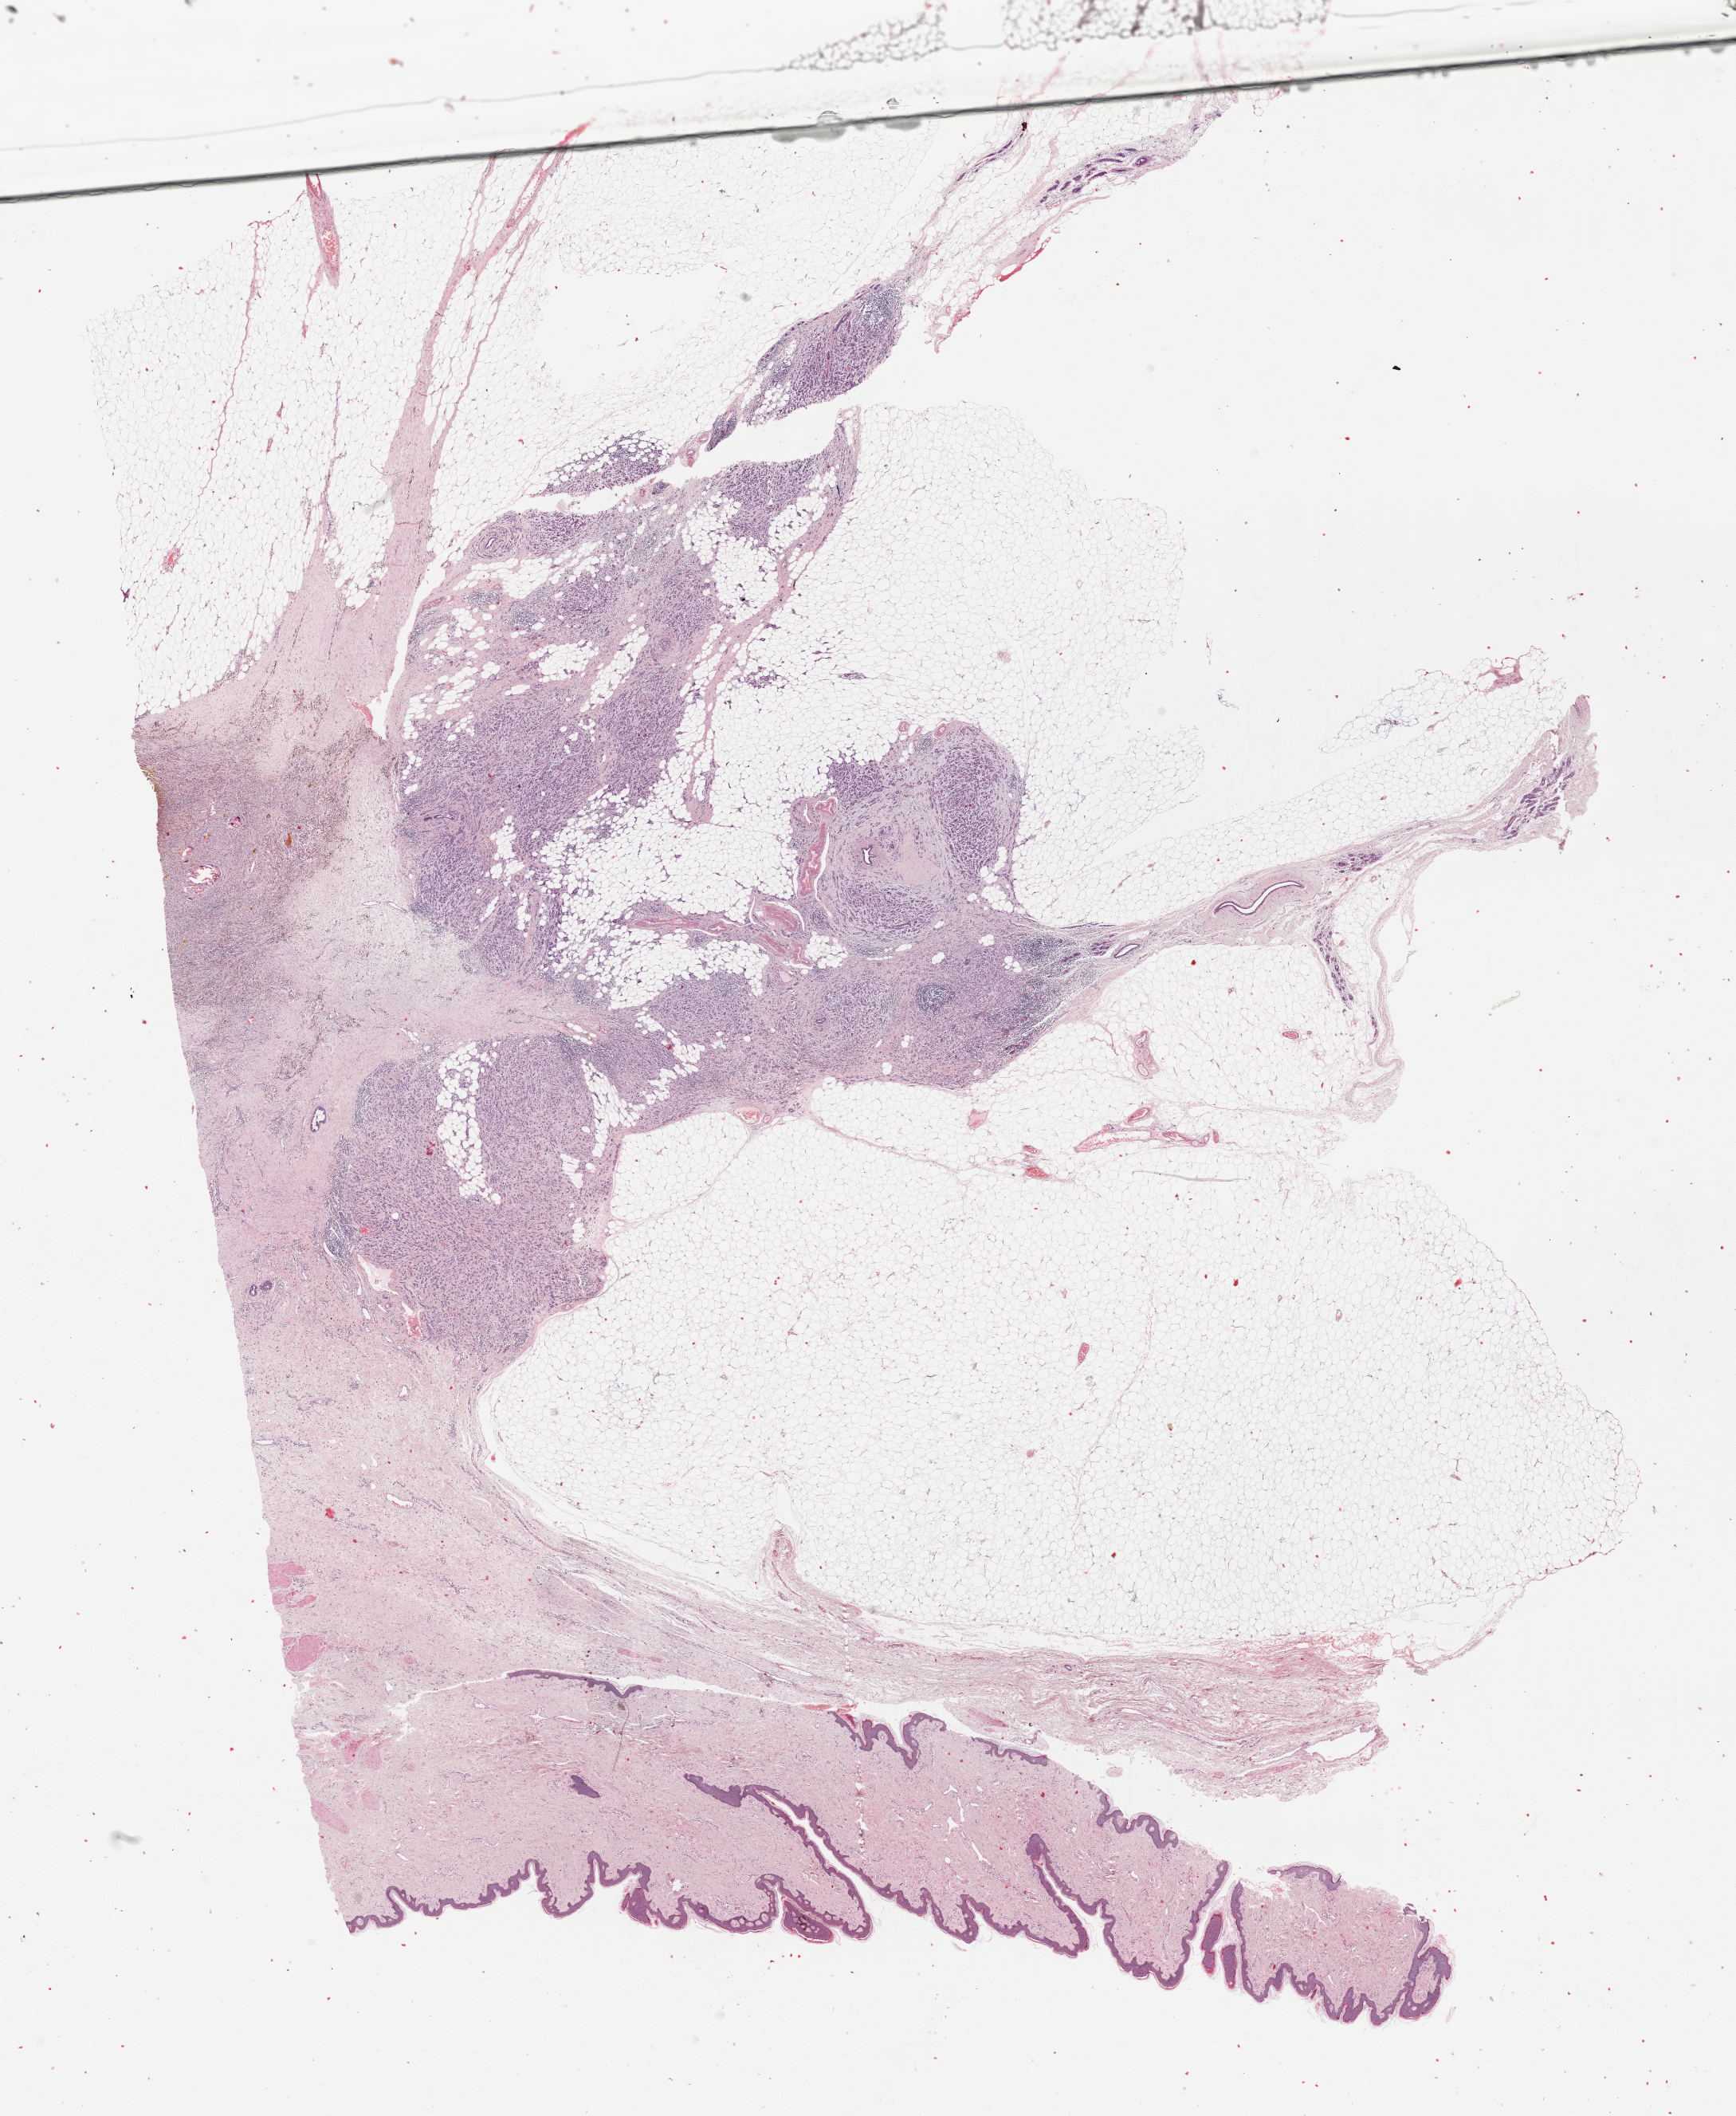
H&E whole-slide image — whole scanned area (about 17.6 x 21.5 mm) shown as a low-resolution overview. Formalin-fixed paraffin-embedded (FFPE) diagnostic section. Sample: primary tumour, breast. Female, age 65 years at initial diagnosis.
- laterality: left
- AJCC pathologic stage: IIIA (7th edition)
- lymph nodes positive (case pathology): 9 of 15 examined
- diagnosis: Infiltrating duct carcinoma, NOS